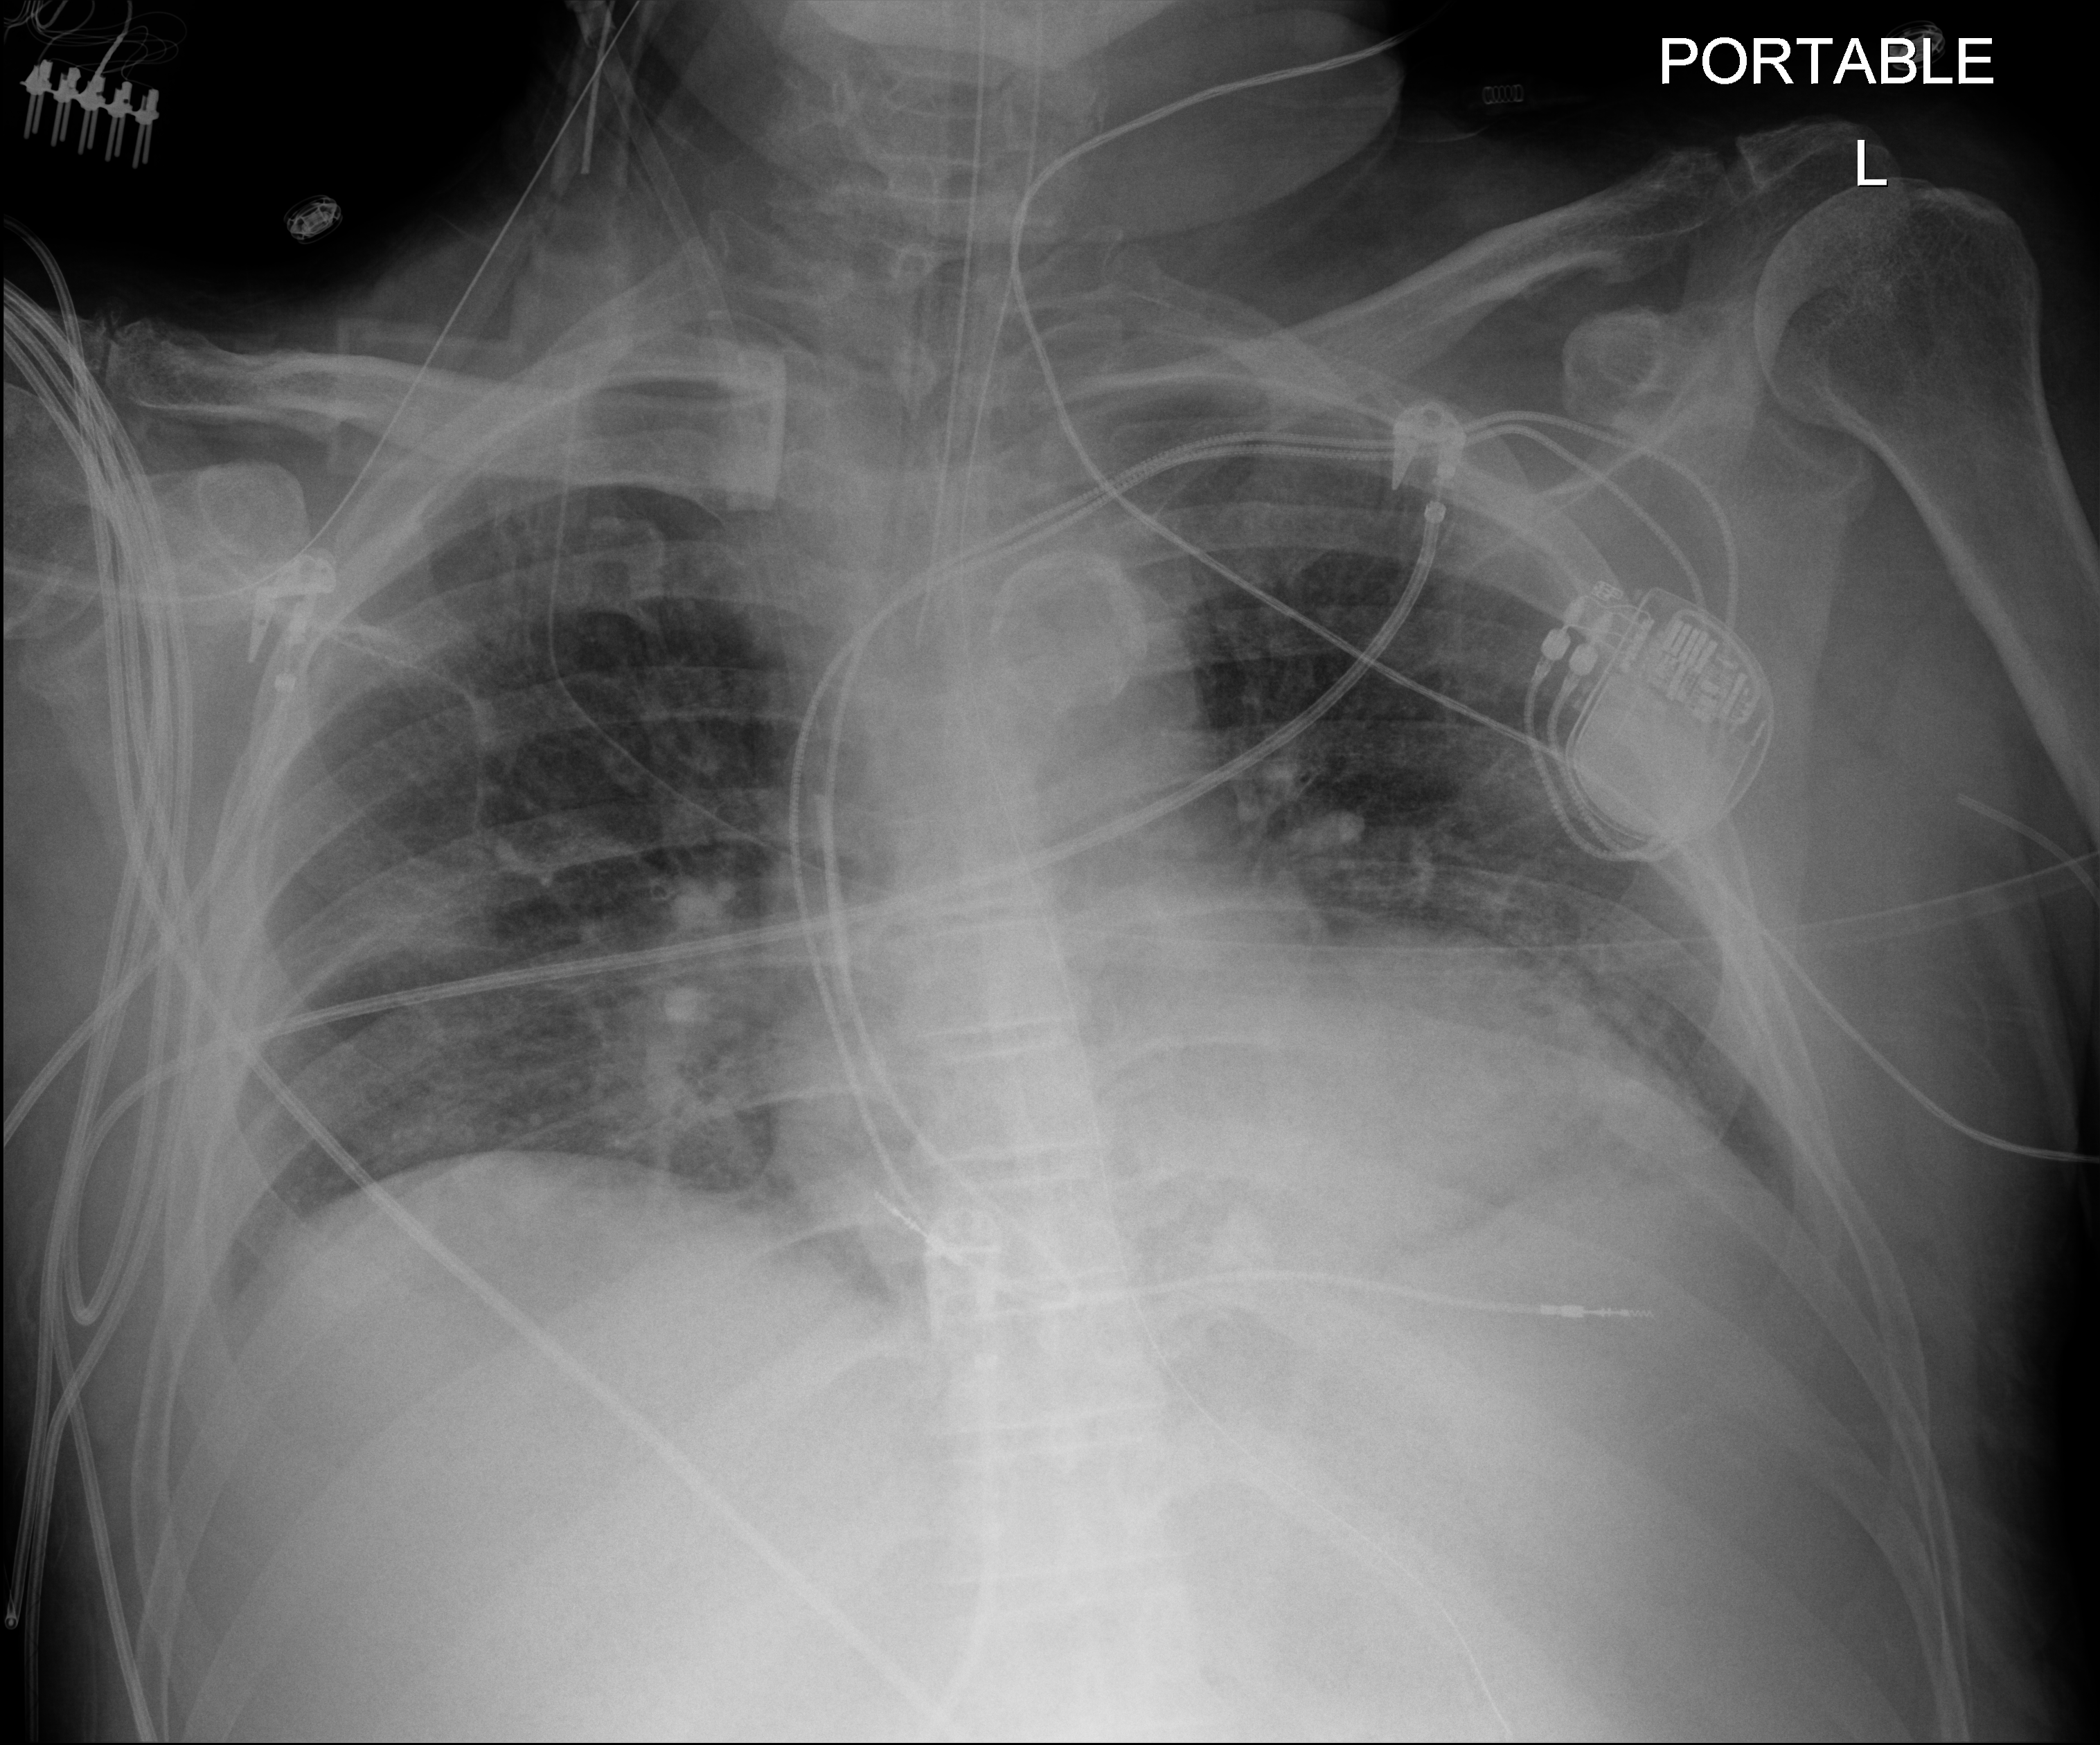
Portable chest radiograph, anteroposterior (AP) projection. Patient hospitalised with COVID-19; male, aged 60–74 years.
From the hospital-stay record, not from the radiograph (when in the stay this image was taken is not recorded):
- admitted to intensive care during this hospital stay: yes
- mechanically ventilated during this hospital stay: yes